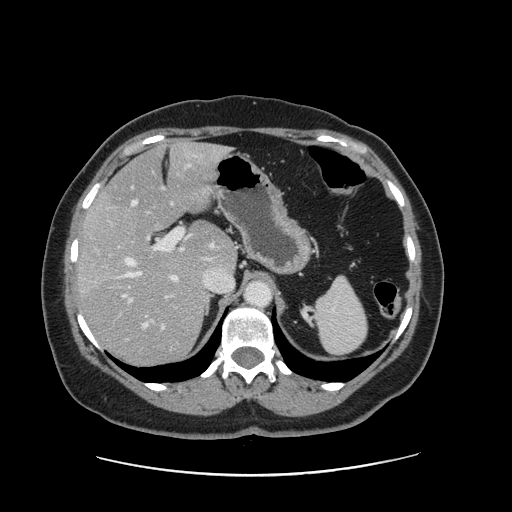
Contrast-enhanced abdominal CT, one axial slice. Position 99 of 161 along the scan axis. Soft-tissue window (W 400 / L 40 HU). 2.5 mm slice thickness. 512 × 512 image matrix, field of view 398 × 398 mm. Female patient, age 62 years. Case-level facts recorded for this patient, not image findings: diagnosis: colorectal cancer liver metastases, imaged before liver resection; multiple liver metastases: no; largest metastasis: 2.5 cm; chemotherapy before resection: yes.
Structures marked on this image (outlined manually by an expert reader):
- hepatic veins: box from (x=124, y=165) to (x=233, y=327) px
- liver: (x=79, y=143)–(x=236, y=364)
- planned liver remnant (the part of the liver to remain after resection): (x=103, y=143)–(x=236, y=270)
- portal vein (with intrahepatic branches): (x=127, y=228)–(x=193, y=331)